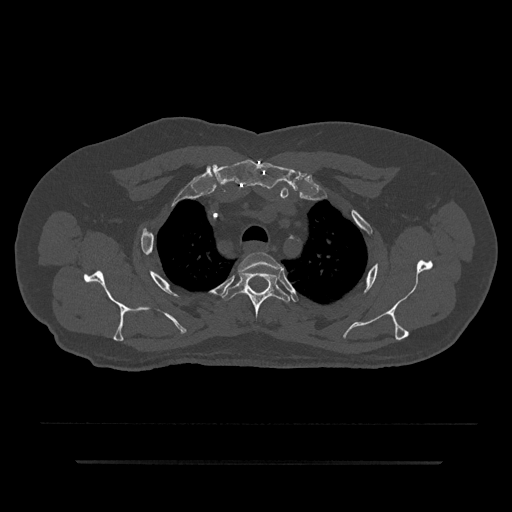
CT including the spine, one axial slice. Slice 668 of 797 in the series (ordered by position). 120 kVp. Bone window (W 1800 / L 400 HU). 0.5 mm slice thickness. 512 × 512 image matrix, field of view 464 × 464 mm. Patient: male, 59 years. From the clinical record (not read from this slice): primary cancer: bile ducts.
Structures marked on this image (semi-automatic segmentation, software-assisted and operator-edited):
- T2 vertebra: bounding box (x1, y1, x2, y2) in pixels: (238, 252, 282, 293)
- T3 vertebra: (223, 269, 290, 320)